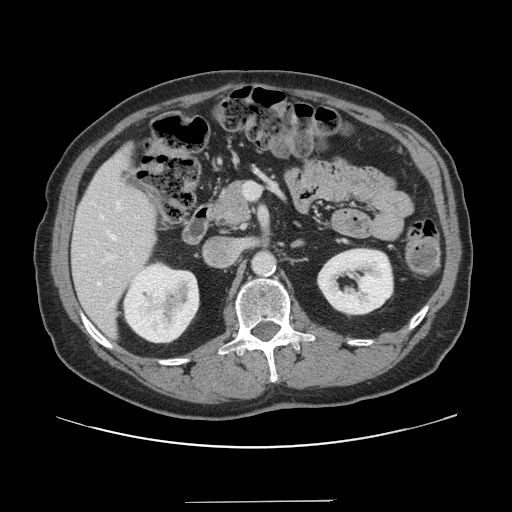
Contrast-enhanced abdominal CT, one axial slice. Slice 70 of 151 in the series (ordered by position). 120 kVp. Intravenous contrast given. Soft-tissue window (W 400 / L 40 HU). 512 × 512 image matrix, field of view 399 × 399 mm. Male patient, age 63 years. Case-level facts recorded for this patient, not image findings: diagnosis: colorectal cancer liver metastases, imaged before liver resection; multiple liver metastases: no; largest metastasis: 2.1 cm.
Outlined on this slice (manually delineated by an expert):
- hepatic veins: box from (x=97, y=202) to (x=119, y=286) px
- liver: (x=73, y=146)–(x=156, y=335)
- planned liver remnant (the part of the liver to remain after resection): (x=73, y=146)–(x=156, y=335)
- portal vein (with intrahepatic branches): (x=102, y=183)–(x=257, y=263)